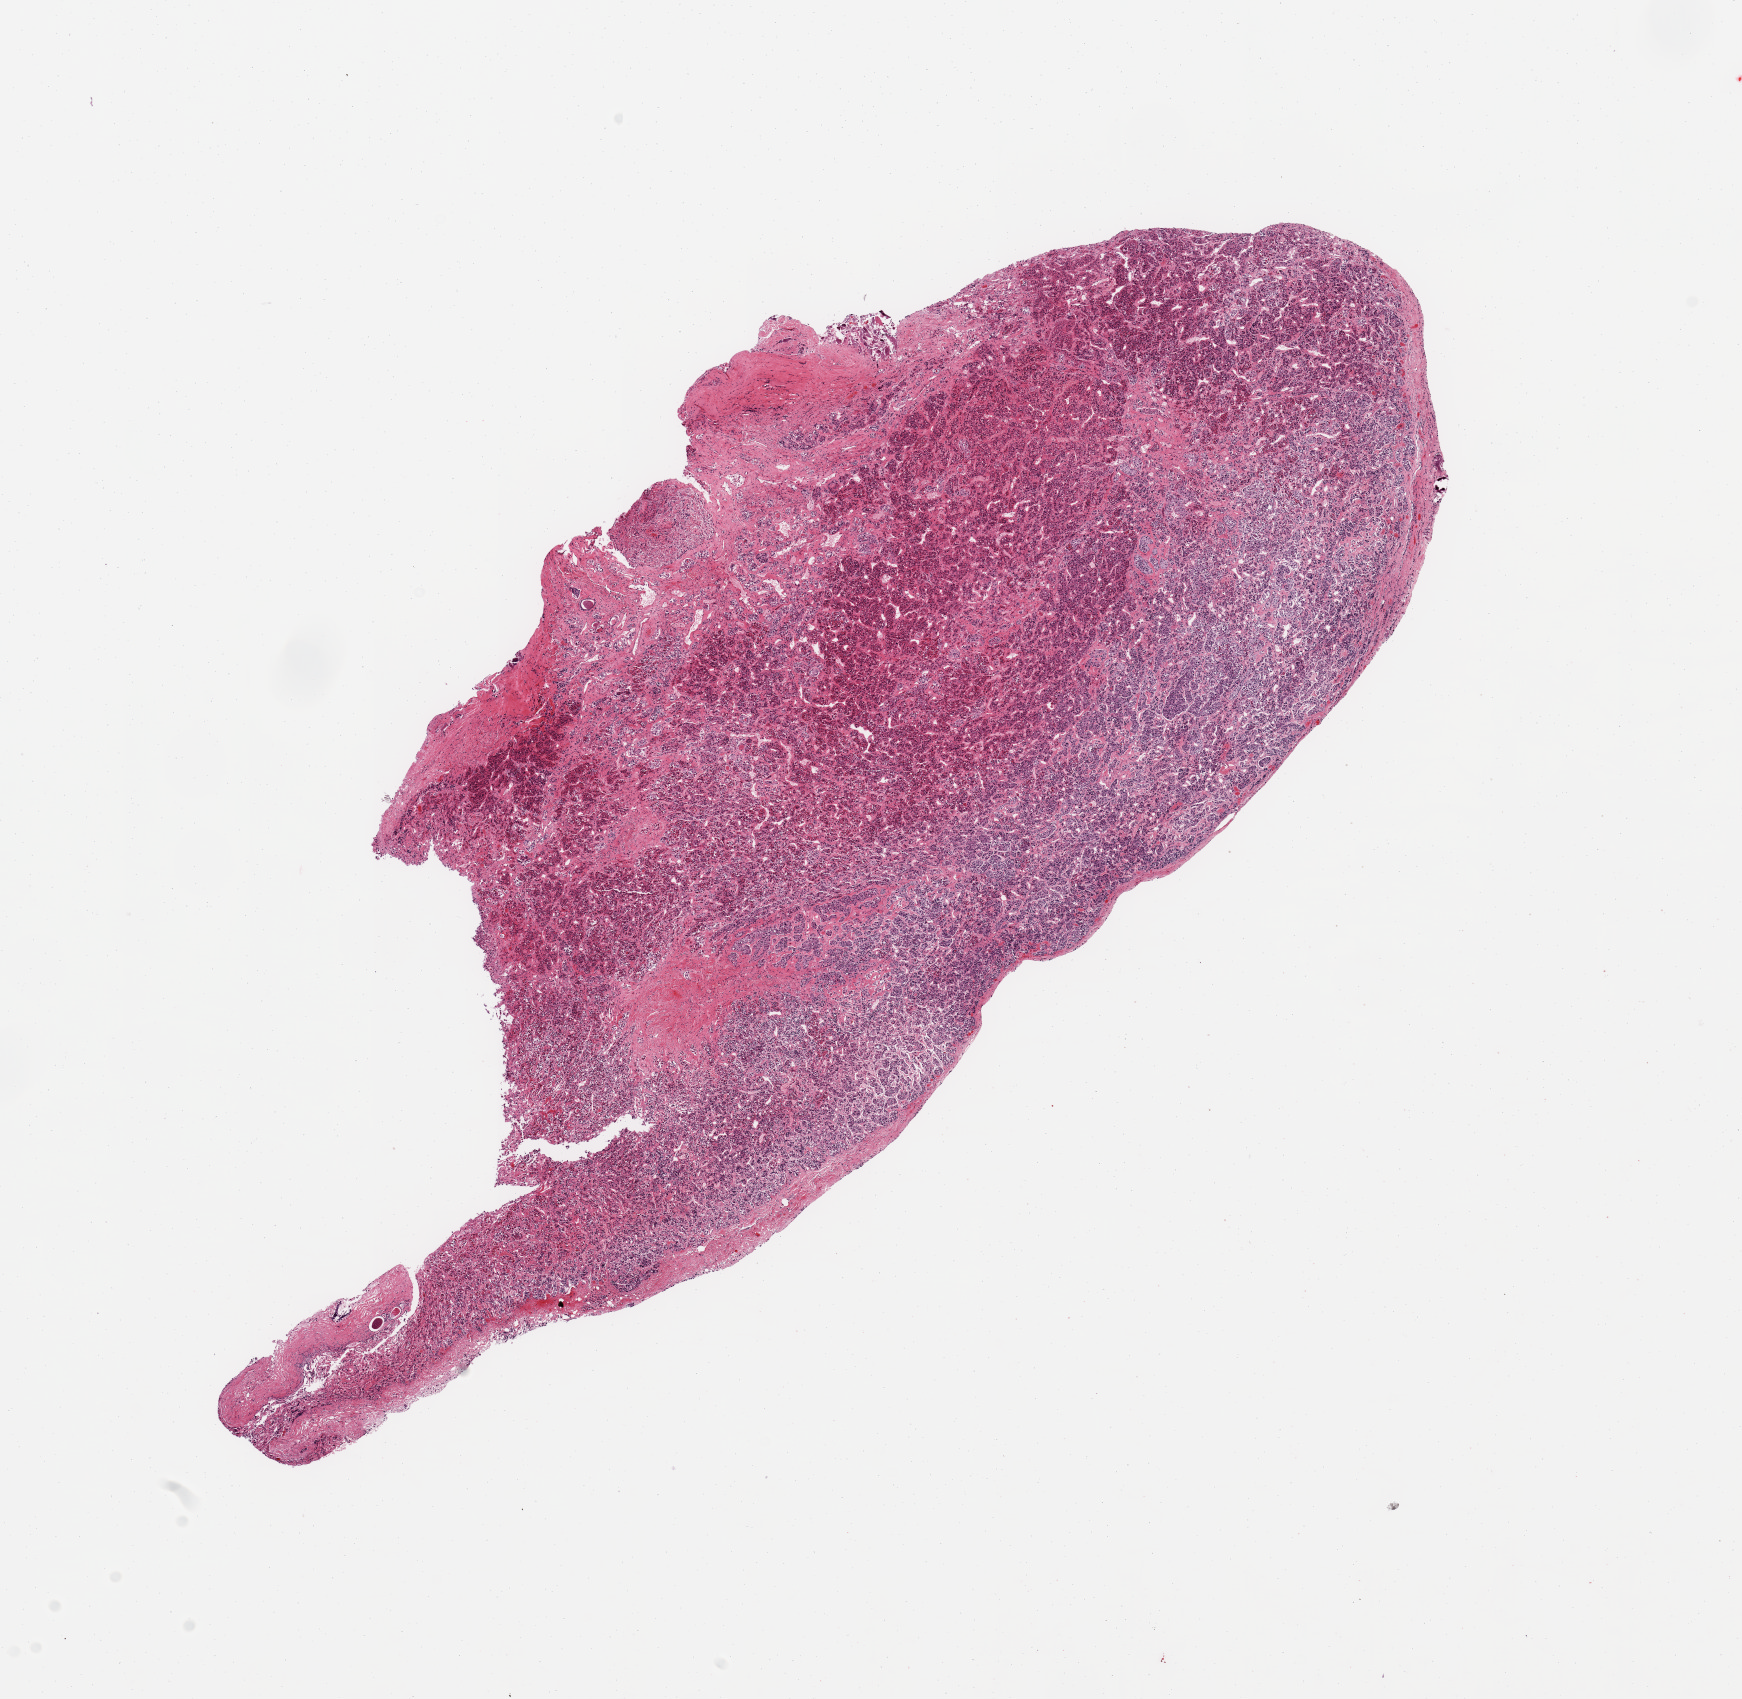
Digitized H&E-stained section, low-resolution overview of the scanned area, about 13.8 x 13.4 mm (slide scanned at 20x). PAXgene-fixed paraffin-embedded (PFPE) section. Section of pituitary (target tissue). Tissue donor sample.
Pathologist's review note for this sample: 1 piece; neural tissue comprises <5%.